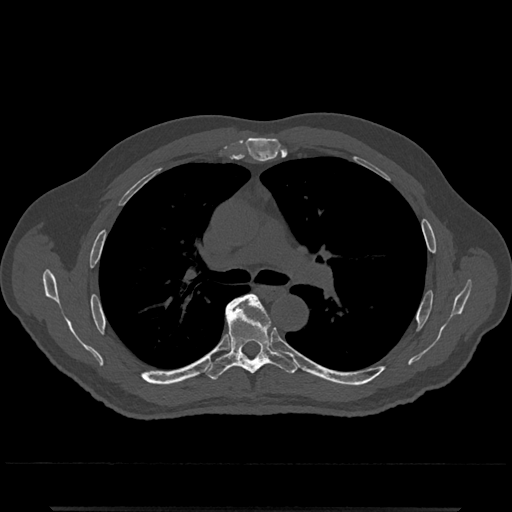
CT including the spine, one axial slice; position 785 of 797 along the scan axis; 120 kVp; bone window (W 1800 / L 400 HU); 0.5 mm slice thickness; 512 × 512 image matrix, field of view 393 × 393 mm. Male patient, age 67 years. From the clinical record (not read from this slice): primary cancer: prostate.
Outlined on this slice (semi-automatically segmented with operator editing):
- T5 vertebra: bounding box <236,295,268,316> (left, top, right, bottom; pixels)
- T6 vertebra: <206,299,298,379>